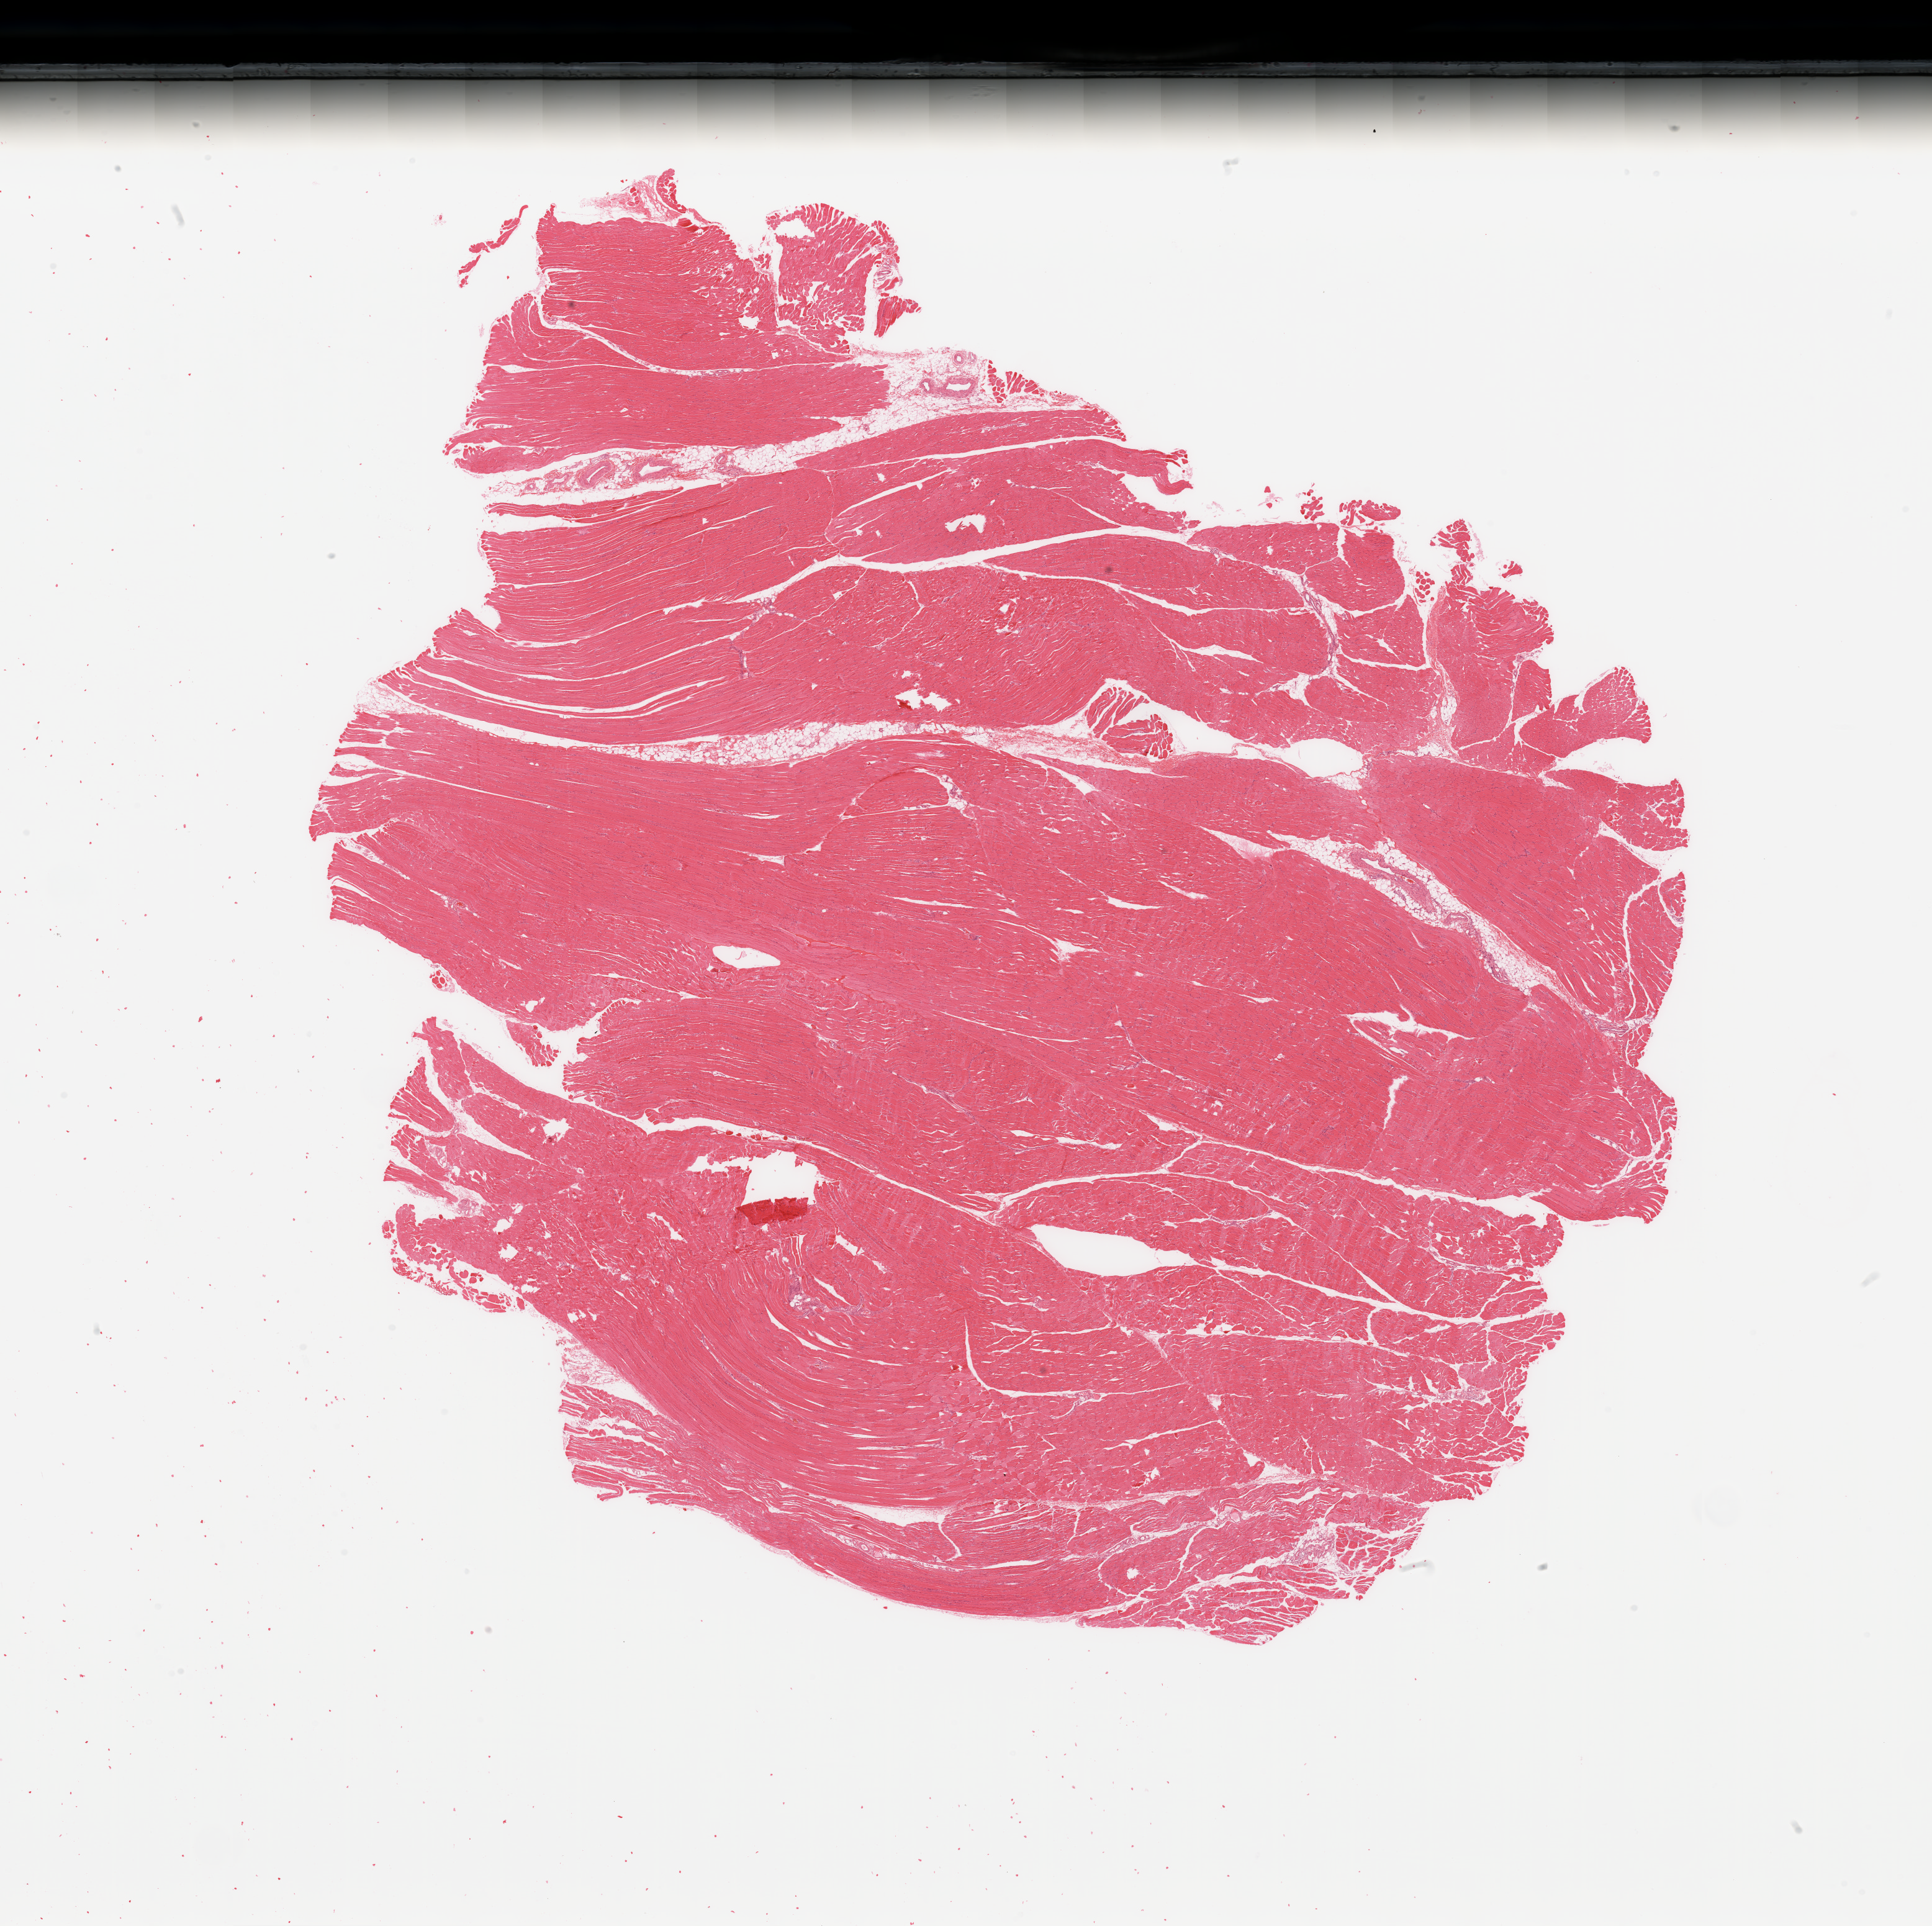
Hematoxylin and eosin (H&E) stained whole-slide image — low-resolution overview of the scanned area, about 24.6 x 24.5 mm (slide scanned at 20x); normal (non-tumour) tissue sample. 32-year-old female patient.
- this section: normal (non-tumour) tissue from the same patient
- patient diagnosis (cohort enrolment): sarcoma (site not recorded at cohort level)